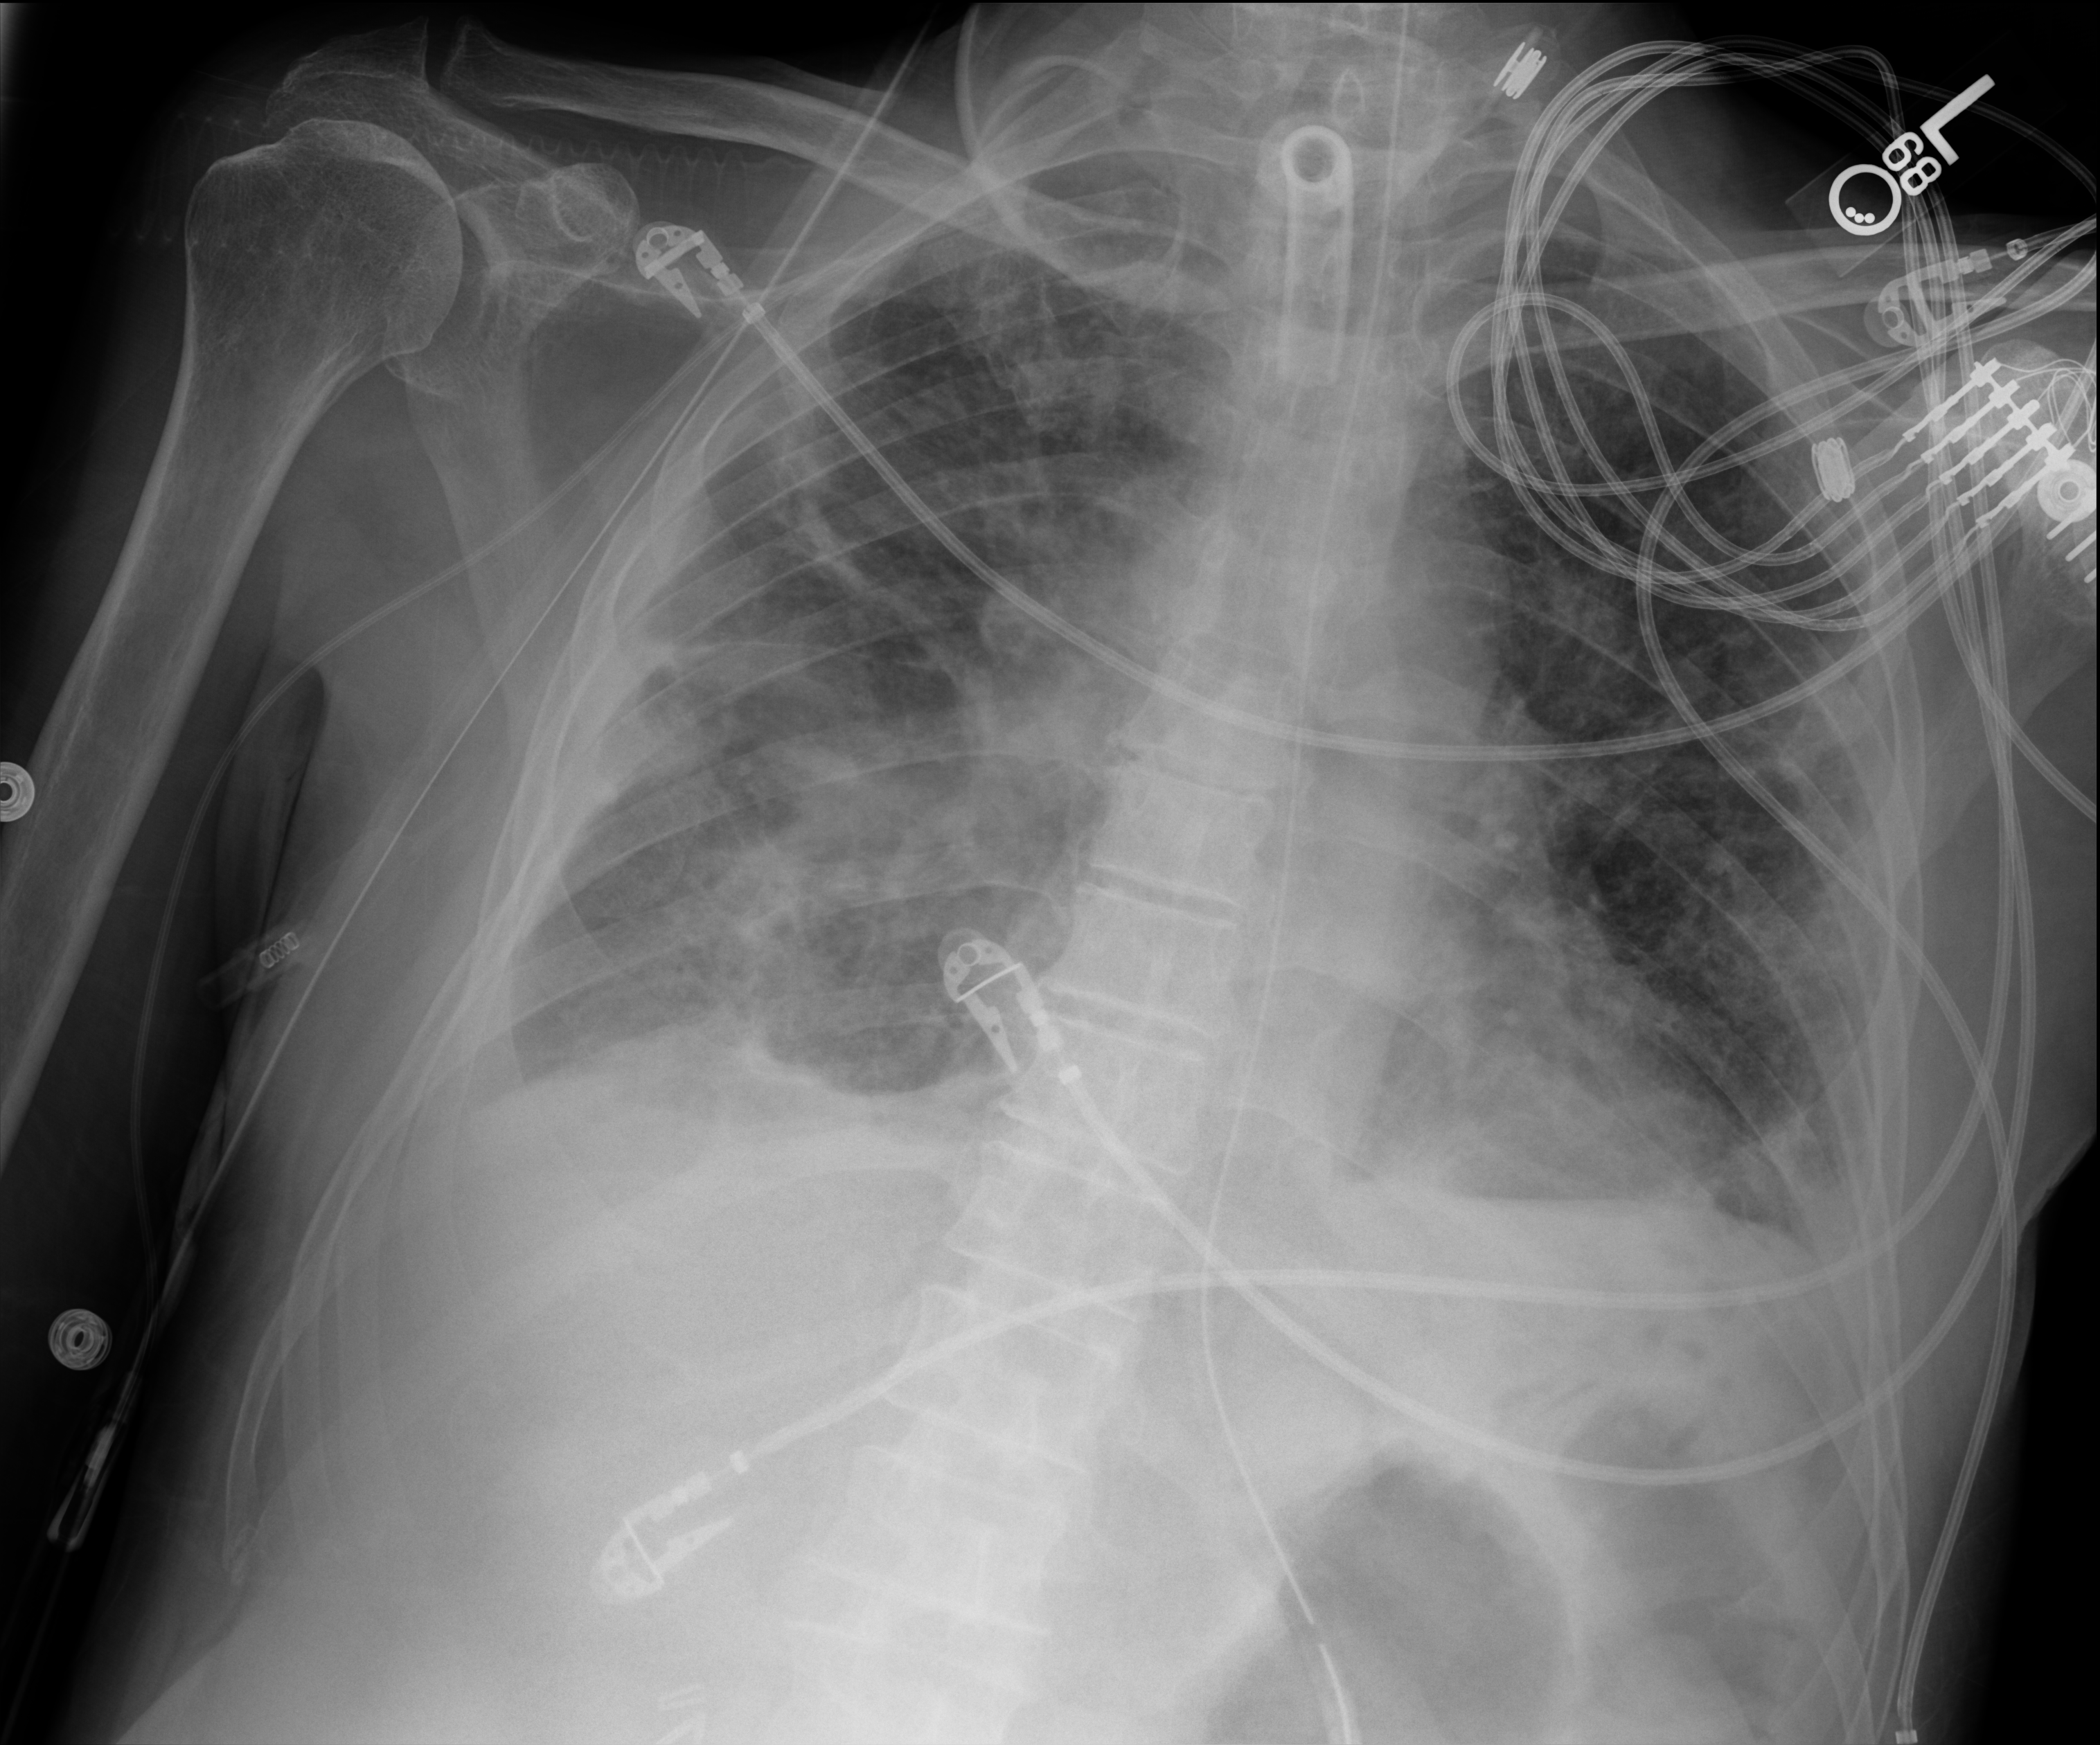
Chest X-ray (portable); anteroposterior (AP) projection. Male patient hospitalised with COVID-19, age 75–90 years.
Admission-level facts for this patient (not findings on this image; timing relative to this image not recorded):
- mechanically ventilated during this hospital stay: yes
- hypertension (admission record): no
- COPD (admission record): no